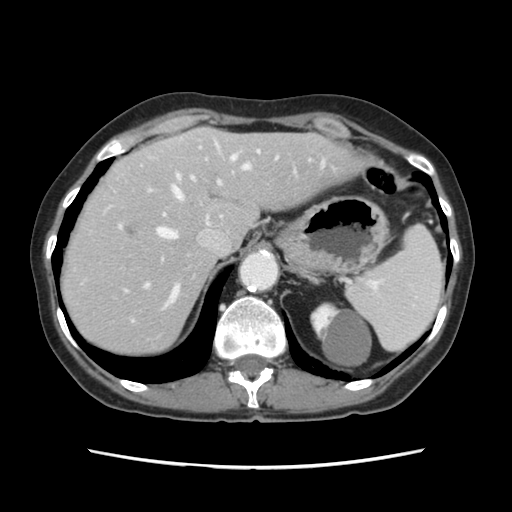
Contrast-enhanced abdominal CT, one axial slice. Position 91 of 120 along the scan axis. 120 kVp. Intravenous contrast given. Soft-tissue window (W 400 / L 40 HU). 2.5 mm slice thickness. 512 × 512 image matrix. Female patient, age 70 years. Case-level facts recorded for this patient, not image findings: diagnosis: colorectal cancer liver metastases, imaged before liver resection; multiple liver metastases: no; largest metastasis: 2.5 cm.
Outlined on this slice (expert manual segmentation):
- hepatic veins: bounding box <158,155,250,309> (left, top, right, bottom; pixels)
- liver: <63,129,358,353>
- planned liver remnant (the part of the liver to remain after resection): <126,129,357,285>
- portal vein (with intrahepatic branches): <119,147,260,288>
- liver metastasis: <126,226,135,235>